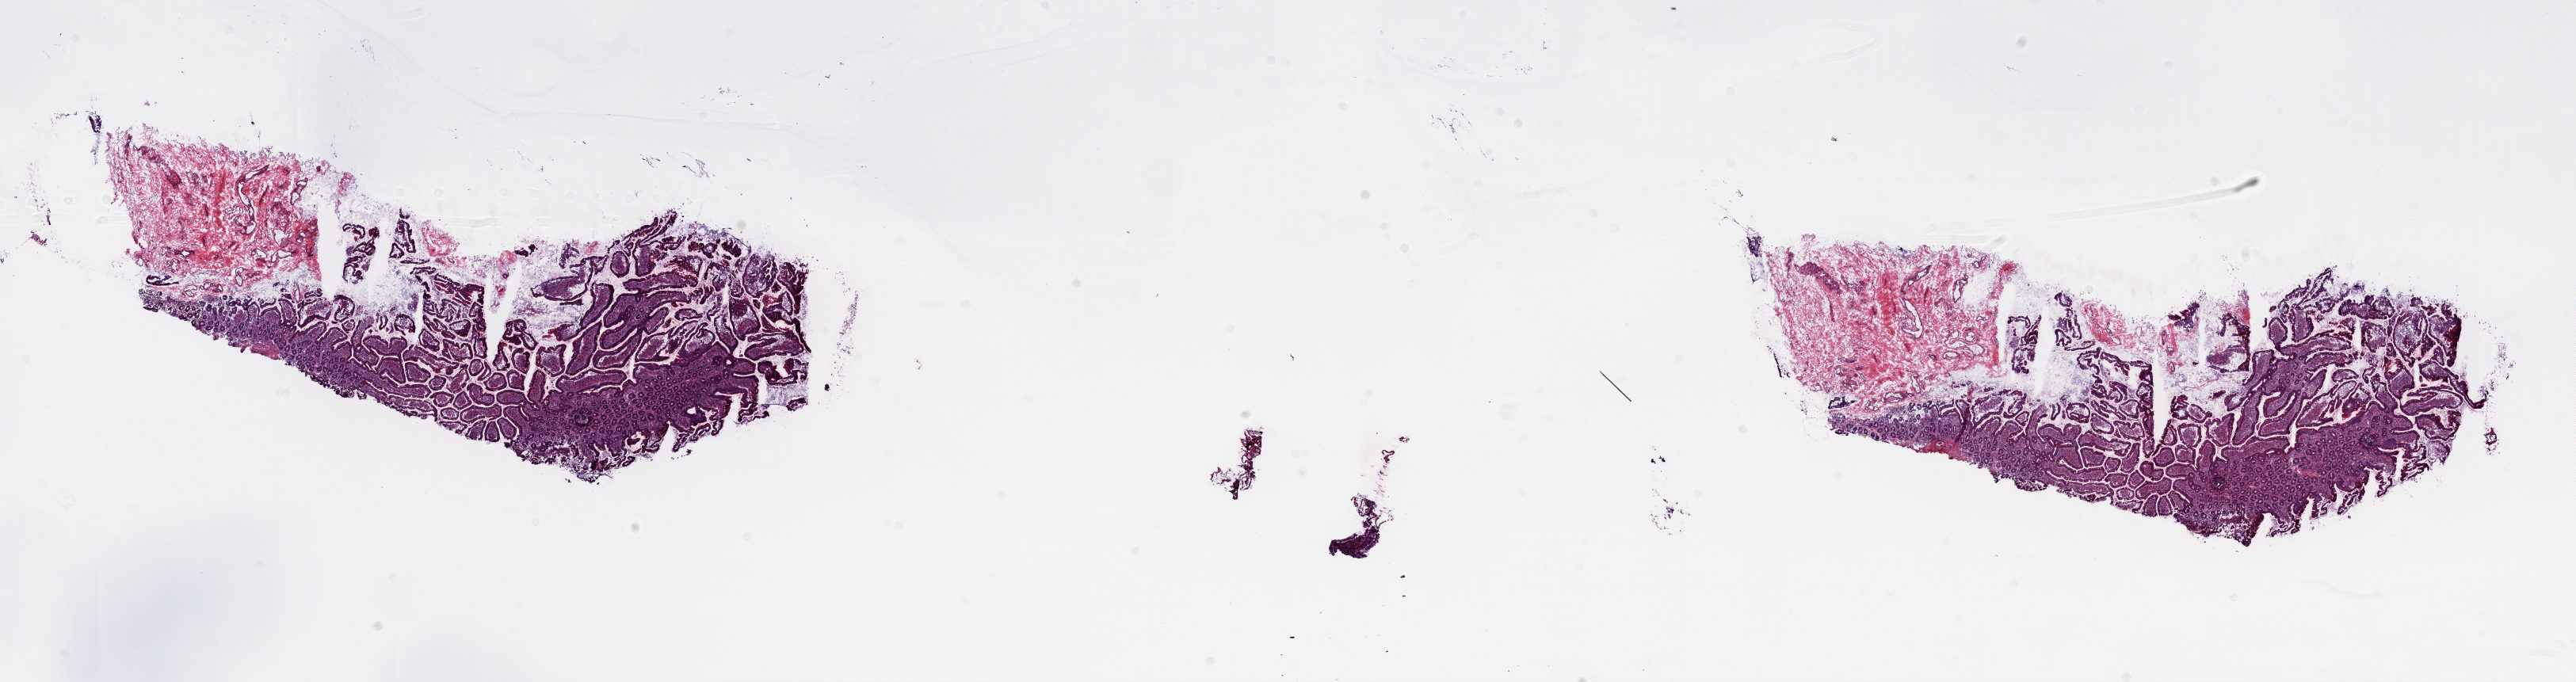
Digitized H&E tissue section (whole slide) — low-resolution overview of the scanned area, about 25.8 x 6.8 mm (from a 20x scan); frozen section from the top of the tissue portion; solid tissue normal (non-tumour tissue) sample from the bile duct. Patient sex: female. Composition of this section per pathologist review: tumour cells 0%, tumour nuclei 0%, normal cells 100%, stromal cells 0%, necrosis 0%. Inflammatory infiltration, as recorded: lymphocyte infiltration 3%, monocyte infiltration 0%, neutrophil infiltration 0%.
* this section: solid tissue normal sample (biorepository sample class)
* patient diagnosis: Cholangiocarcinoma (head of pancreas)